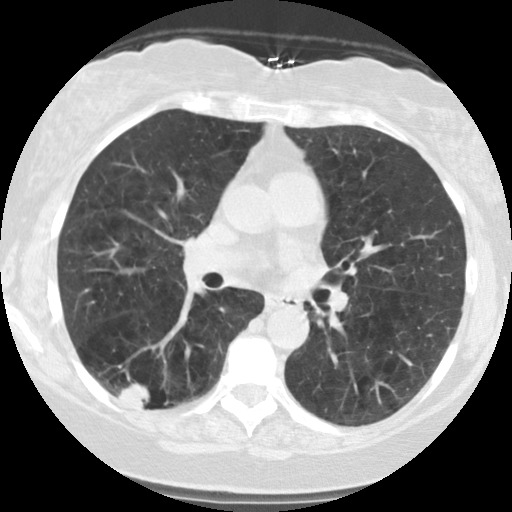
Low-dose screening chest CT, axial slice, second annual screen, lung window (W 1500 / L -600 HU), 2.5 mm slice thickness. Female participant, aged 59 years at enrolment.
Lesion marked by an expert reader, bounding box <106,361,179,422> (left, top, right, bottom; pixels). The screening reader recorded 2 non-calcified nodules or masses ≥4 mm on this exam; which of them this box marks is not recorded. Participant outcome: lung cancer diagnosed 63 days after this screen — squamous cell carcinoma, NOS, right lower lobe, poorly differentiated (G3), stage IB (AJCC 6th edition), 30 mm at pathology.